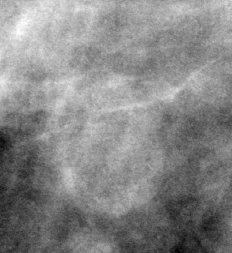
Cropped region of a digitized screen-film mammogram centred on a radiologist-marked abnormality; right breast; MLO view.
- Finding: mass, shape oval, margins circumscribed; BI-RADS assessment category 3; benign without callback (not worked up further).